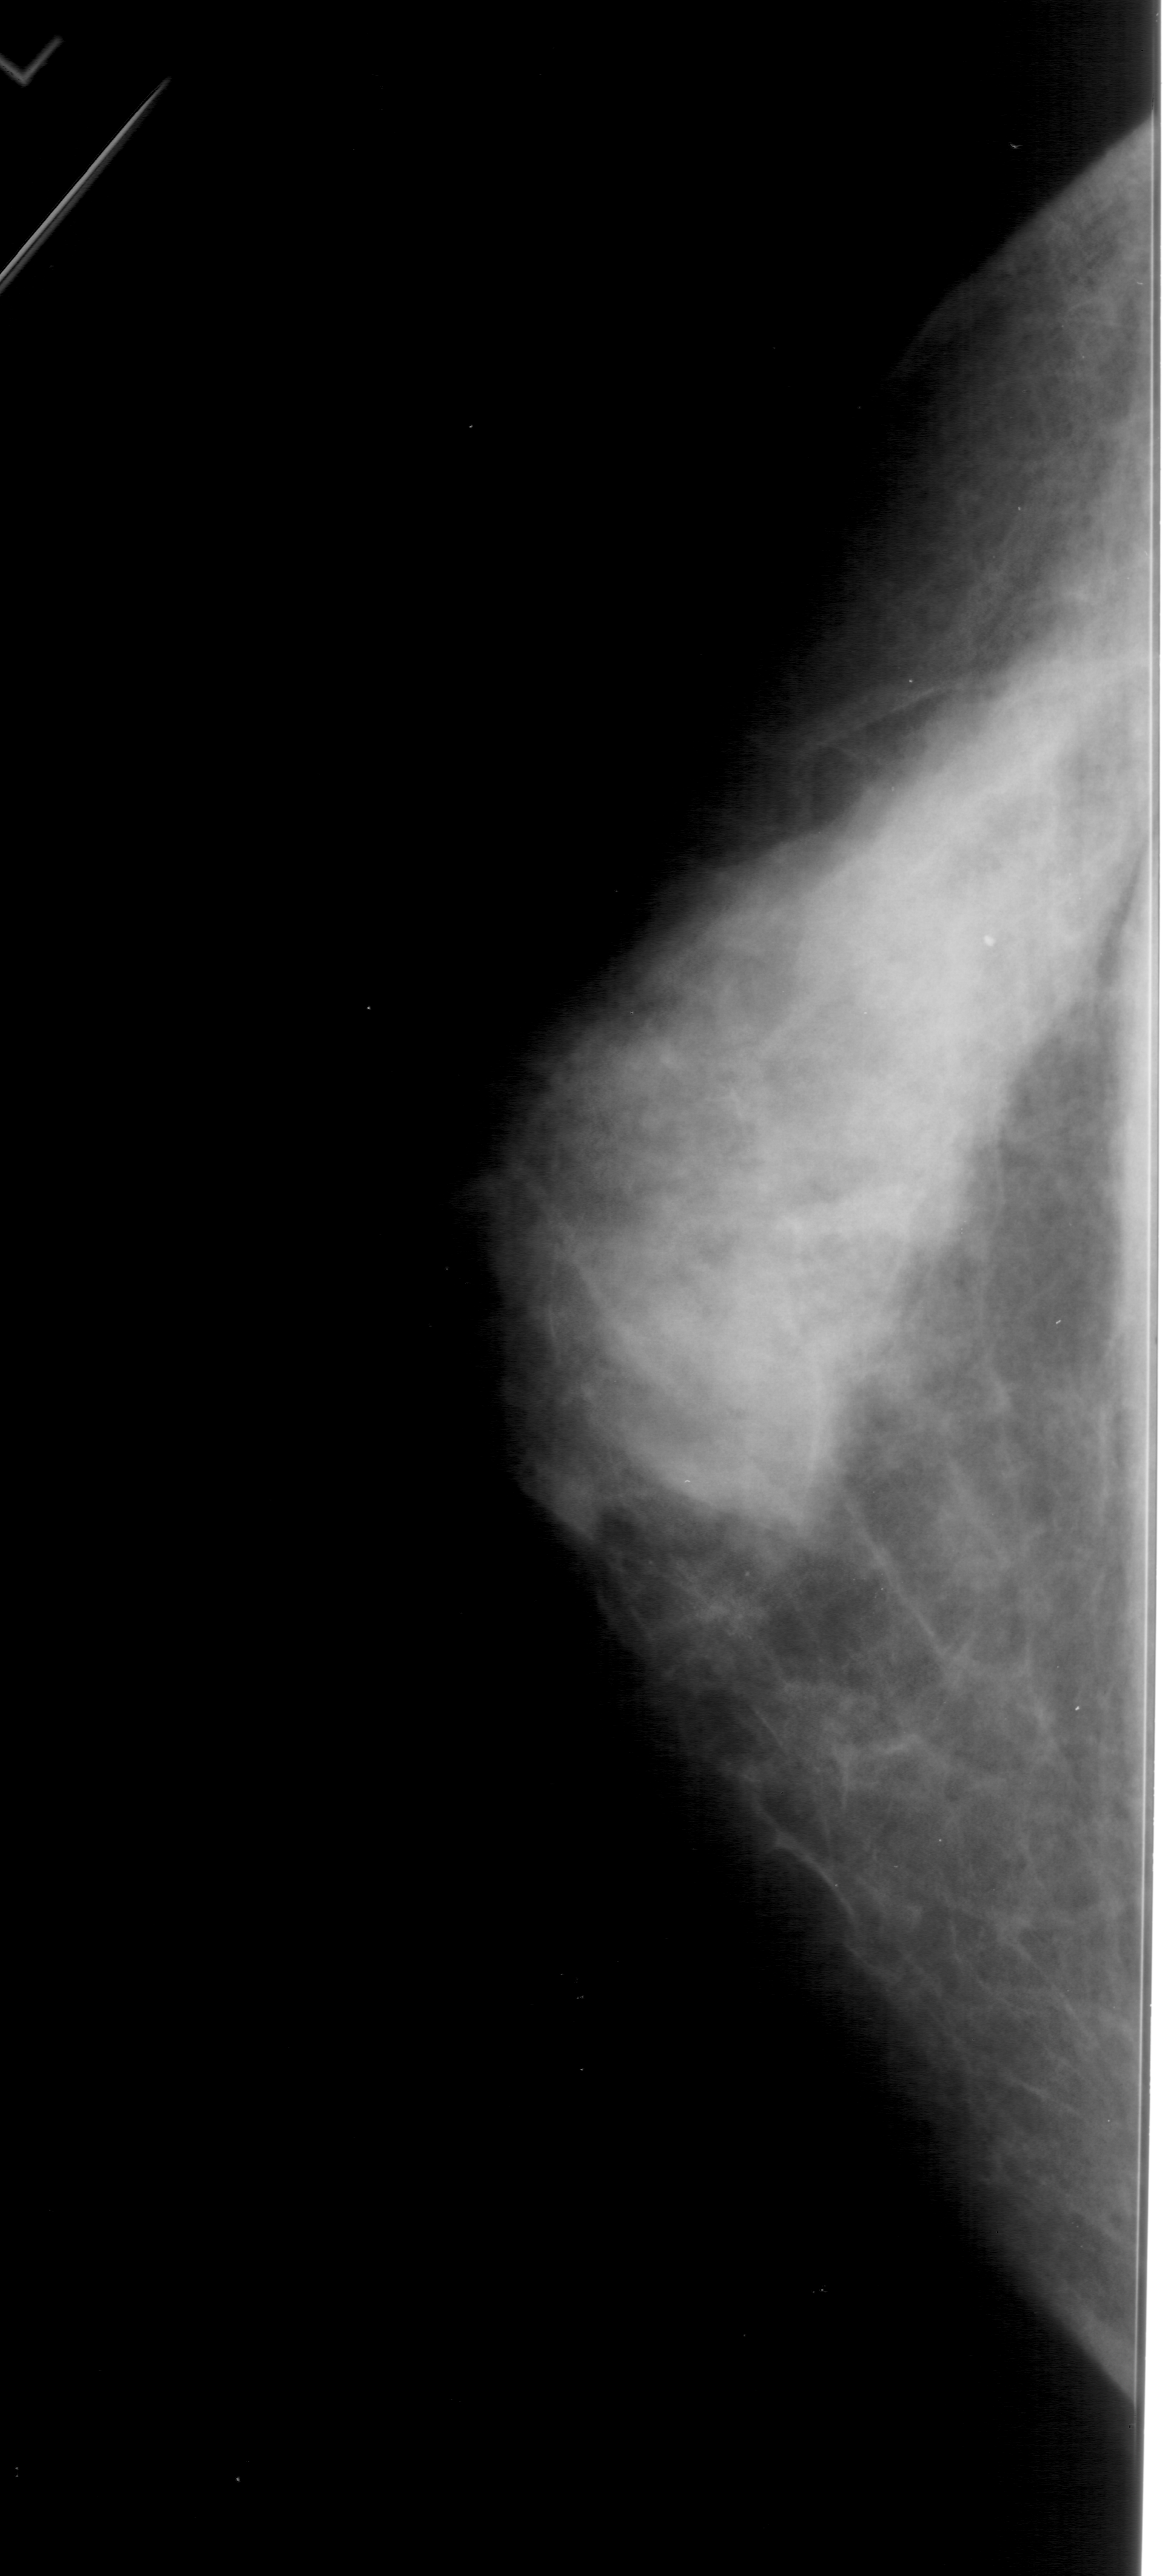
Mammogram (digitized film); left breast; craniocaudal (CC) view; breast composition: extremely dense (BI-RADS density category 4 of 4); 1165 × 2576 image matrix.
Marked abnormalities (boxes around the expert regions of interest):
- calcifications, morphology amorphous, distribution clustered; BI-RADS assessment category 4; pathology result (as recorded, not read from the image): benign: bounding box (x1, y1, x2, y2) in pixels: (552, 1459, 835, 1684)